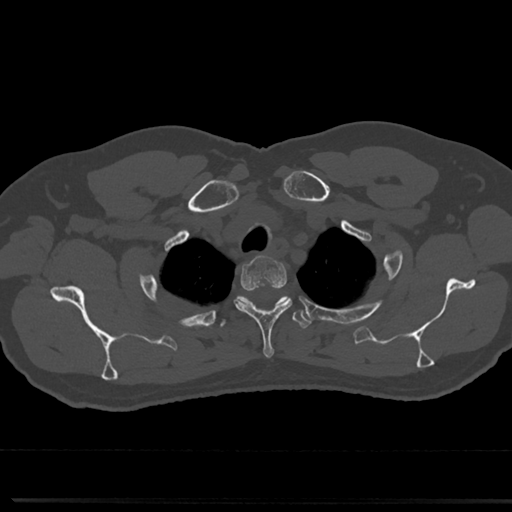
CT including the spine, one axial slice; position 622 of 817 along the scan axis; bone window (W 1800 / L 400 HU); 0.5 mm slice thickness; 512 × 512 image matrix, field of view 355 × 355 mm. Male patient, age 61 years. Case-level facts recorded for this patient, not image findings: primary cancer: prostate.
Annotated regions visible in this slice (semi-automatic segmentation, software-assisted and operator-edited):
- T2 vertebra: bounding box <234,259,289,355> (left, top, right, bottom; pixels)
- T3 vertebra: <216,294,313,332>